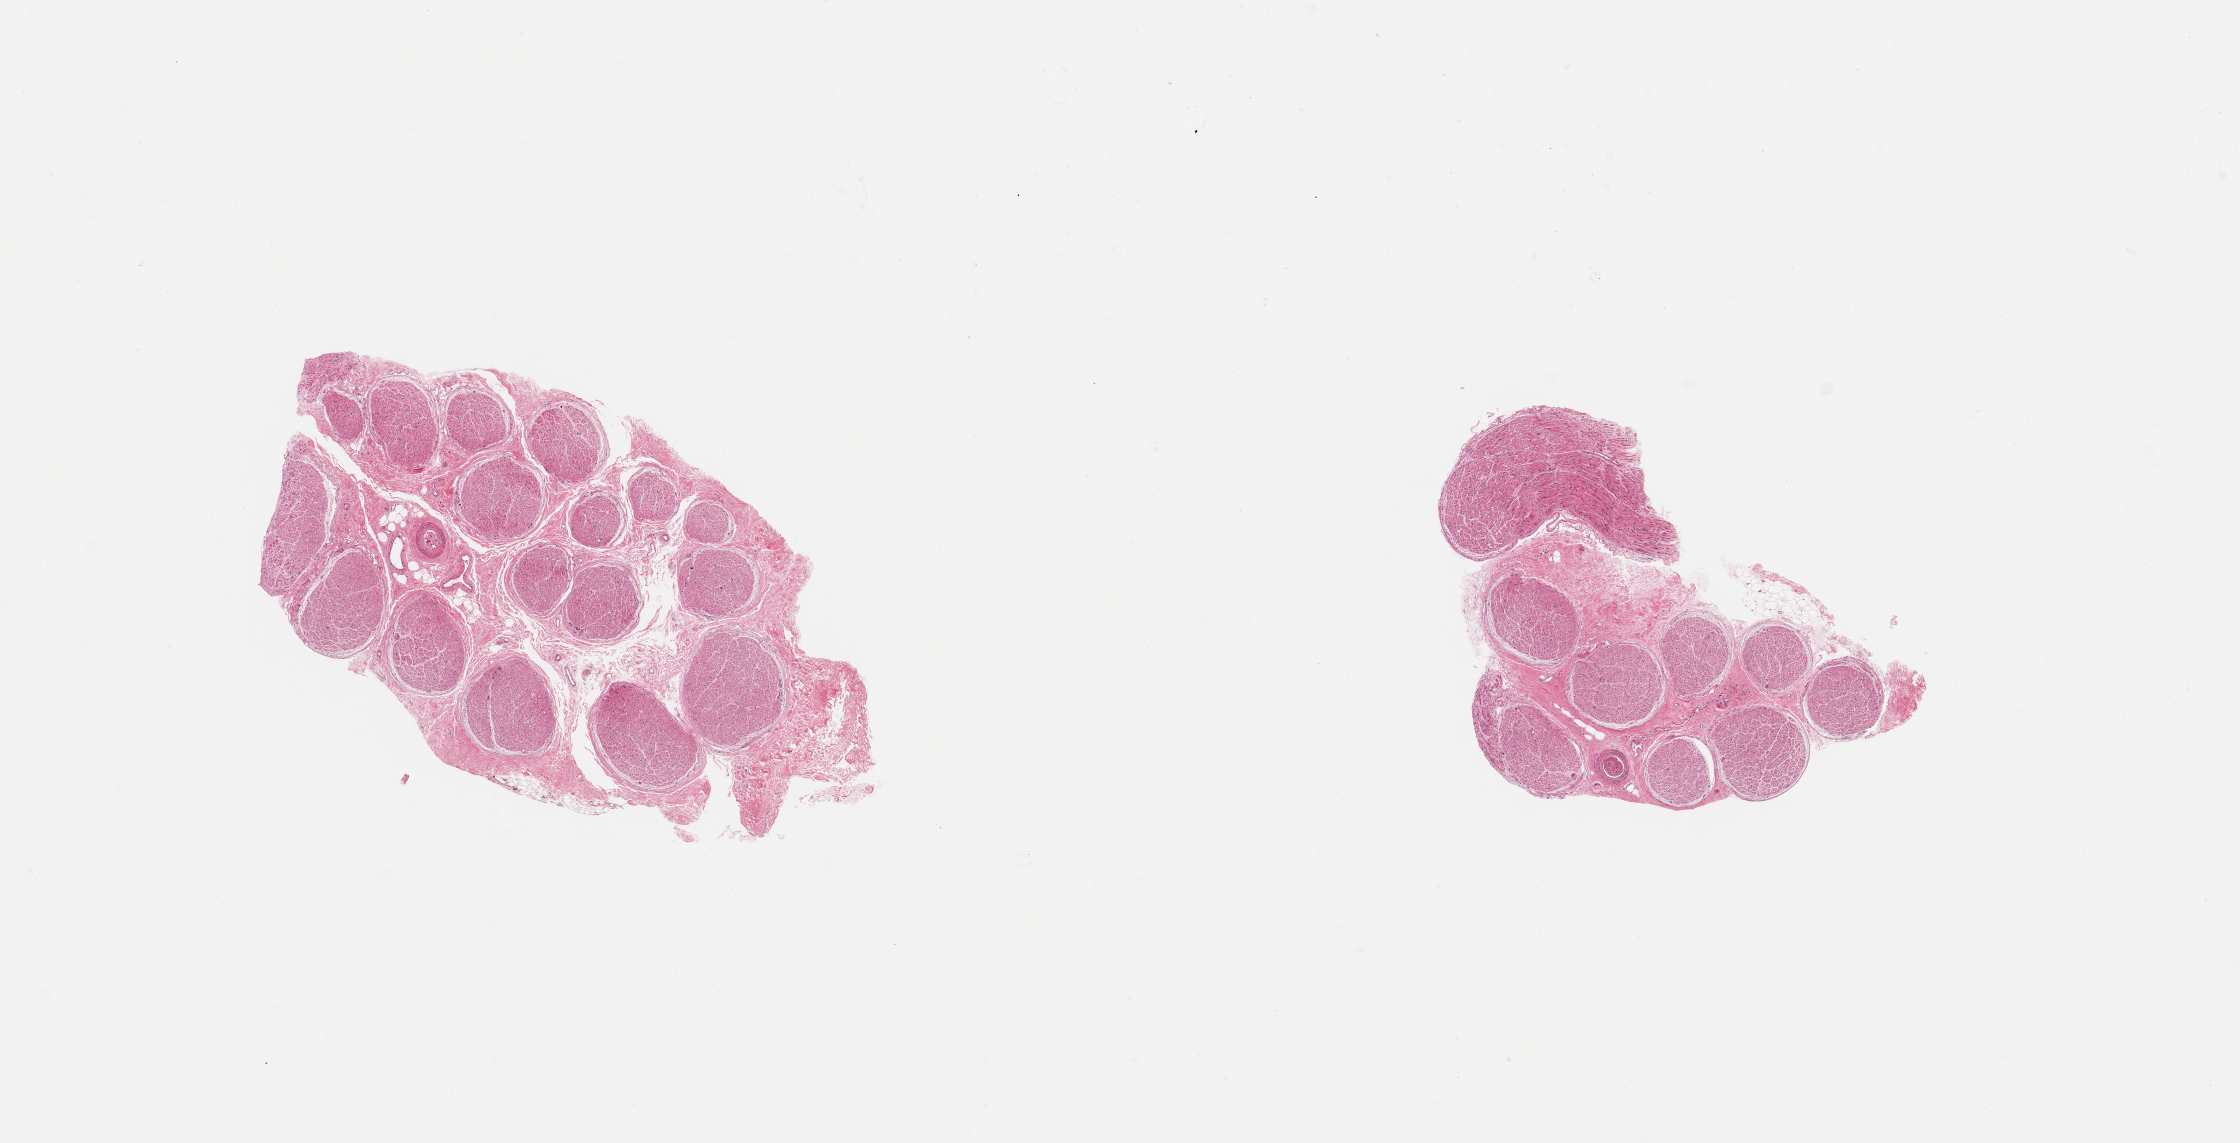
Digitized H&E-stained section — shown as a low-resolution overview of the whole scanned area (about 17.7 x 9.0 mm). PAXgene-fixed paraffin-embedded (PFPE) section. Section of tibial nerve (target tissue). Tissue donor sample.
Pathologist's review note for this sample: 2 pieces; insignificant amount of internal/external fat.